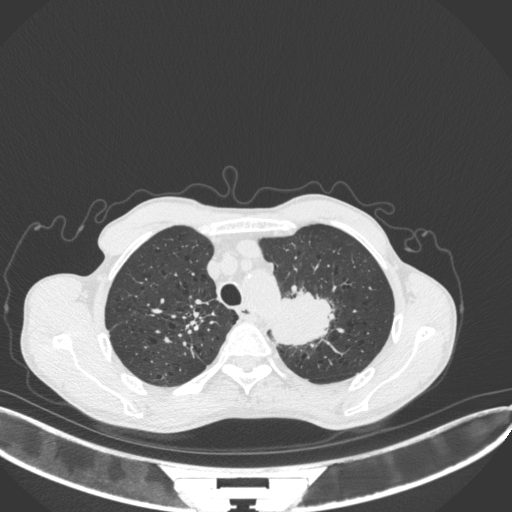
Chest CT, one axial slice. 120 kVp. Lung window (W 1500 / L -600 HU). 1 mm slice thickness. 512 × 512 image matrix. Male patient, age 65 years. From the clinical record (not read from this slice): clinical TNM (as recorded): T2b N0 M0; histopathological grade: G2.
Outlined on this slice (bounding box drawn by a radiologist):
- lung tumour (recorded histology: adenocarcinoma): bounding box (x1, y1, x2, y2) in pixels: (267, 286, 336, 346)